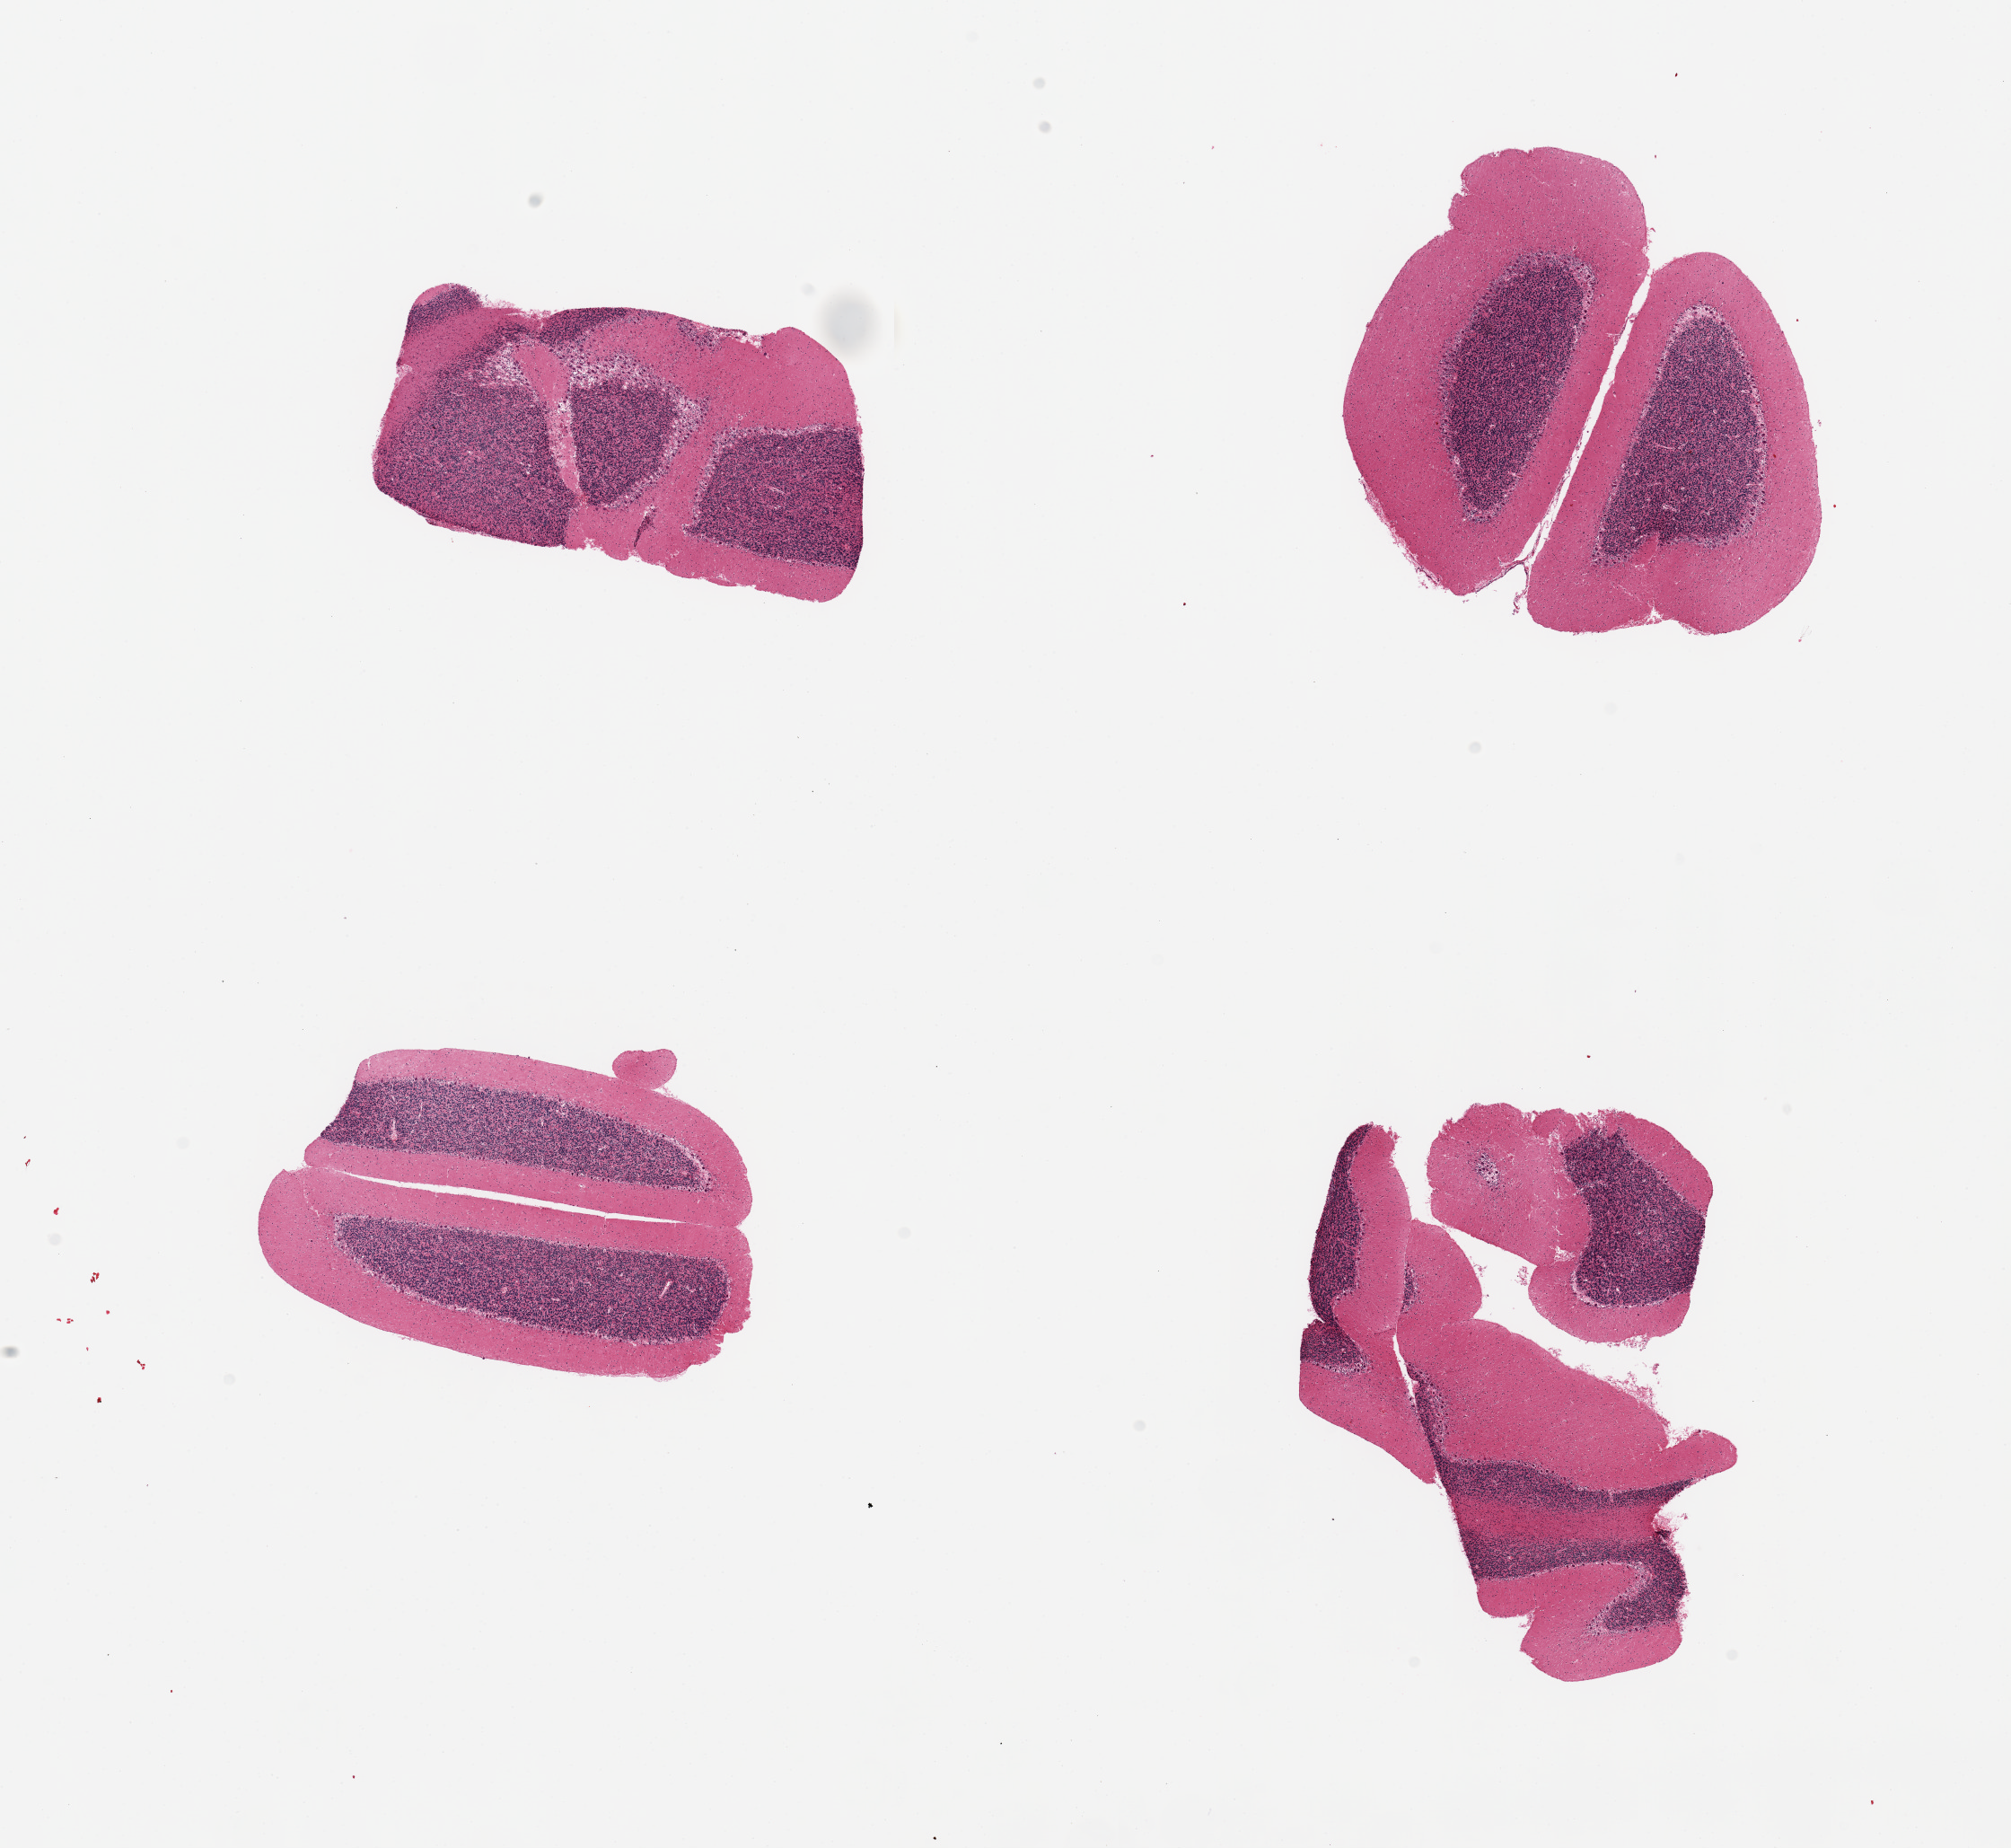
Whole-slide image, hematoxylin and eosin (H&E) stain, brightfield — a low-resolution overview of the entire scanned area, about 17.7 x 16.3 mm (slide scanned at 20x); PAXgene-fixed, paraffin-embedded tissue; sampled site (target tissue): cerebellum; tissue donor sample. Donor: female.
* pathologist's review note for this sample: 4 pieces, no significant abnormalities